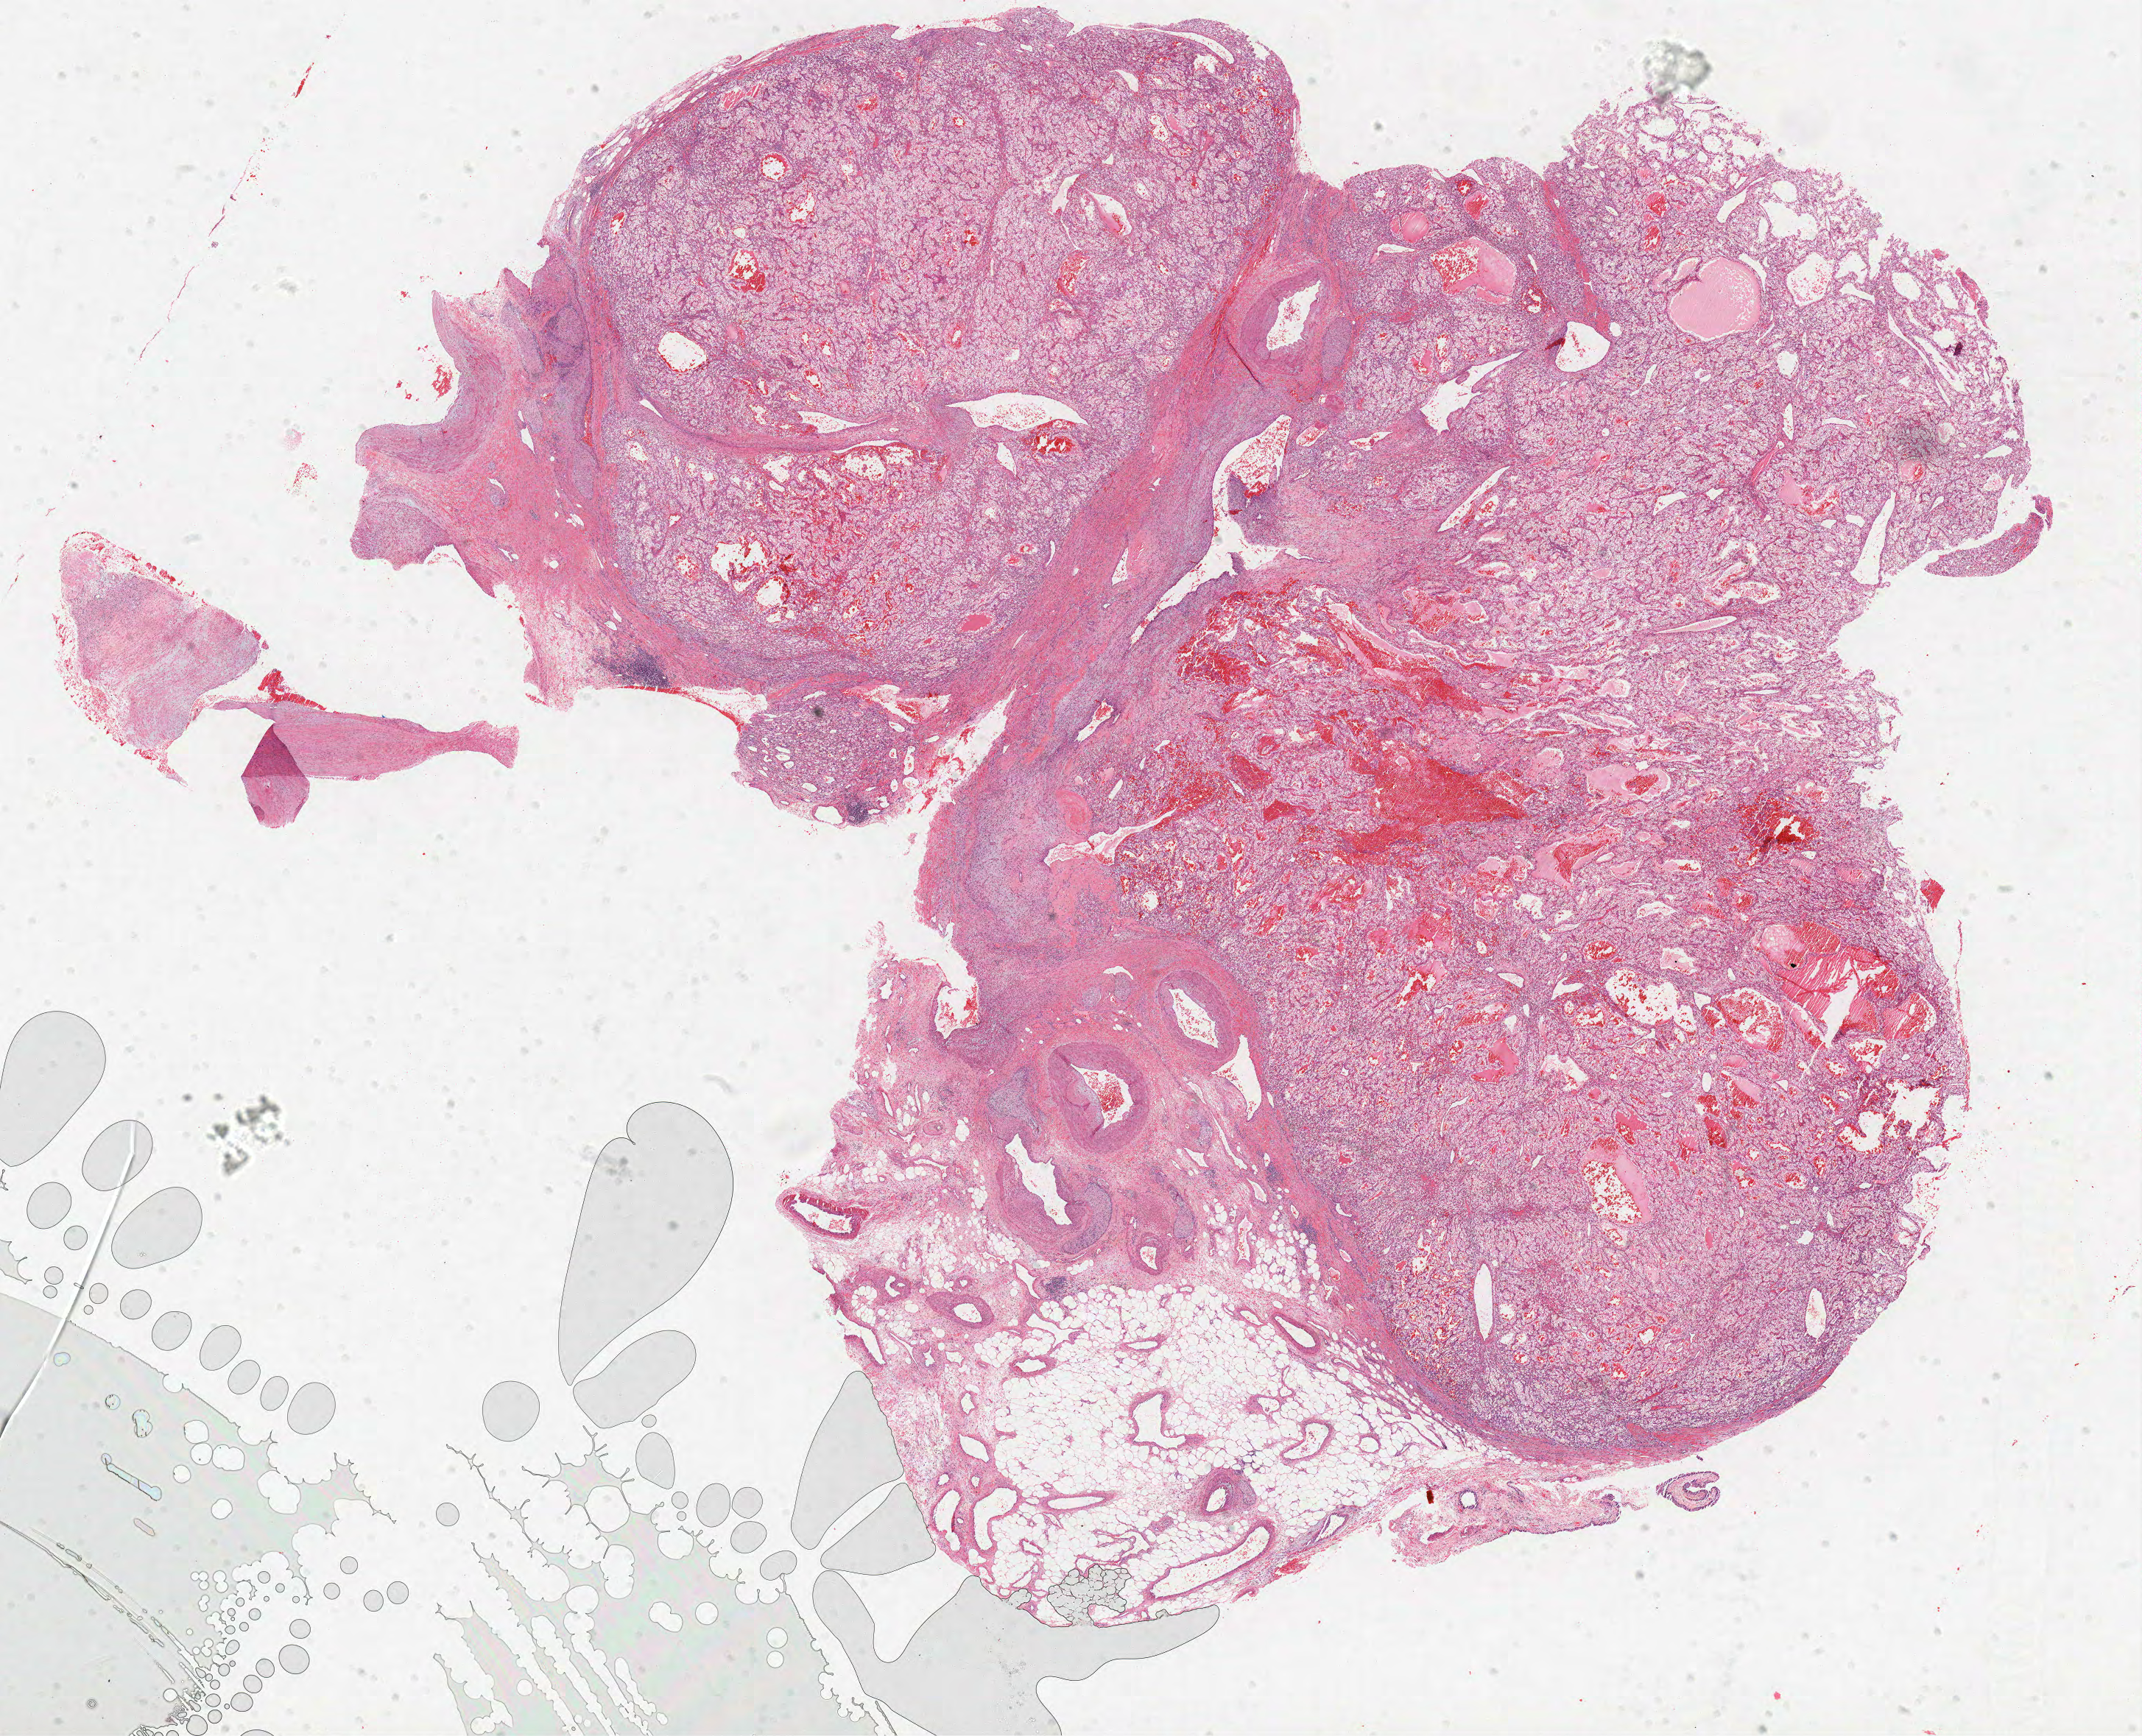
Digitized Hematoxylin and eosin (H&E) stained tissue section (whole slide), low-resolution overview of the scanned area, about 23.3 x 18.9 mm (from a 40x scan), formalin-fixed paraffin-embedded (FFPE) diagnostic section, sample: primary tumour, kidney. Male patient; age at initial diagnosis 70 years. Histologic grade: G2 (moderately differentiated).
• AJCC pathologic stage: I
• histologic diagnosis: Clear cell adenocarcinoma, NOS